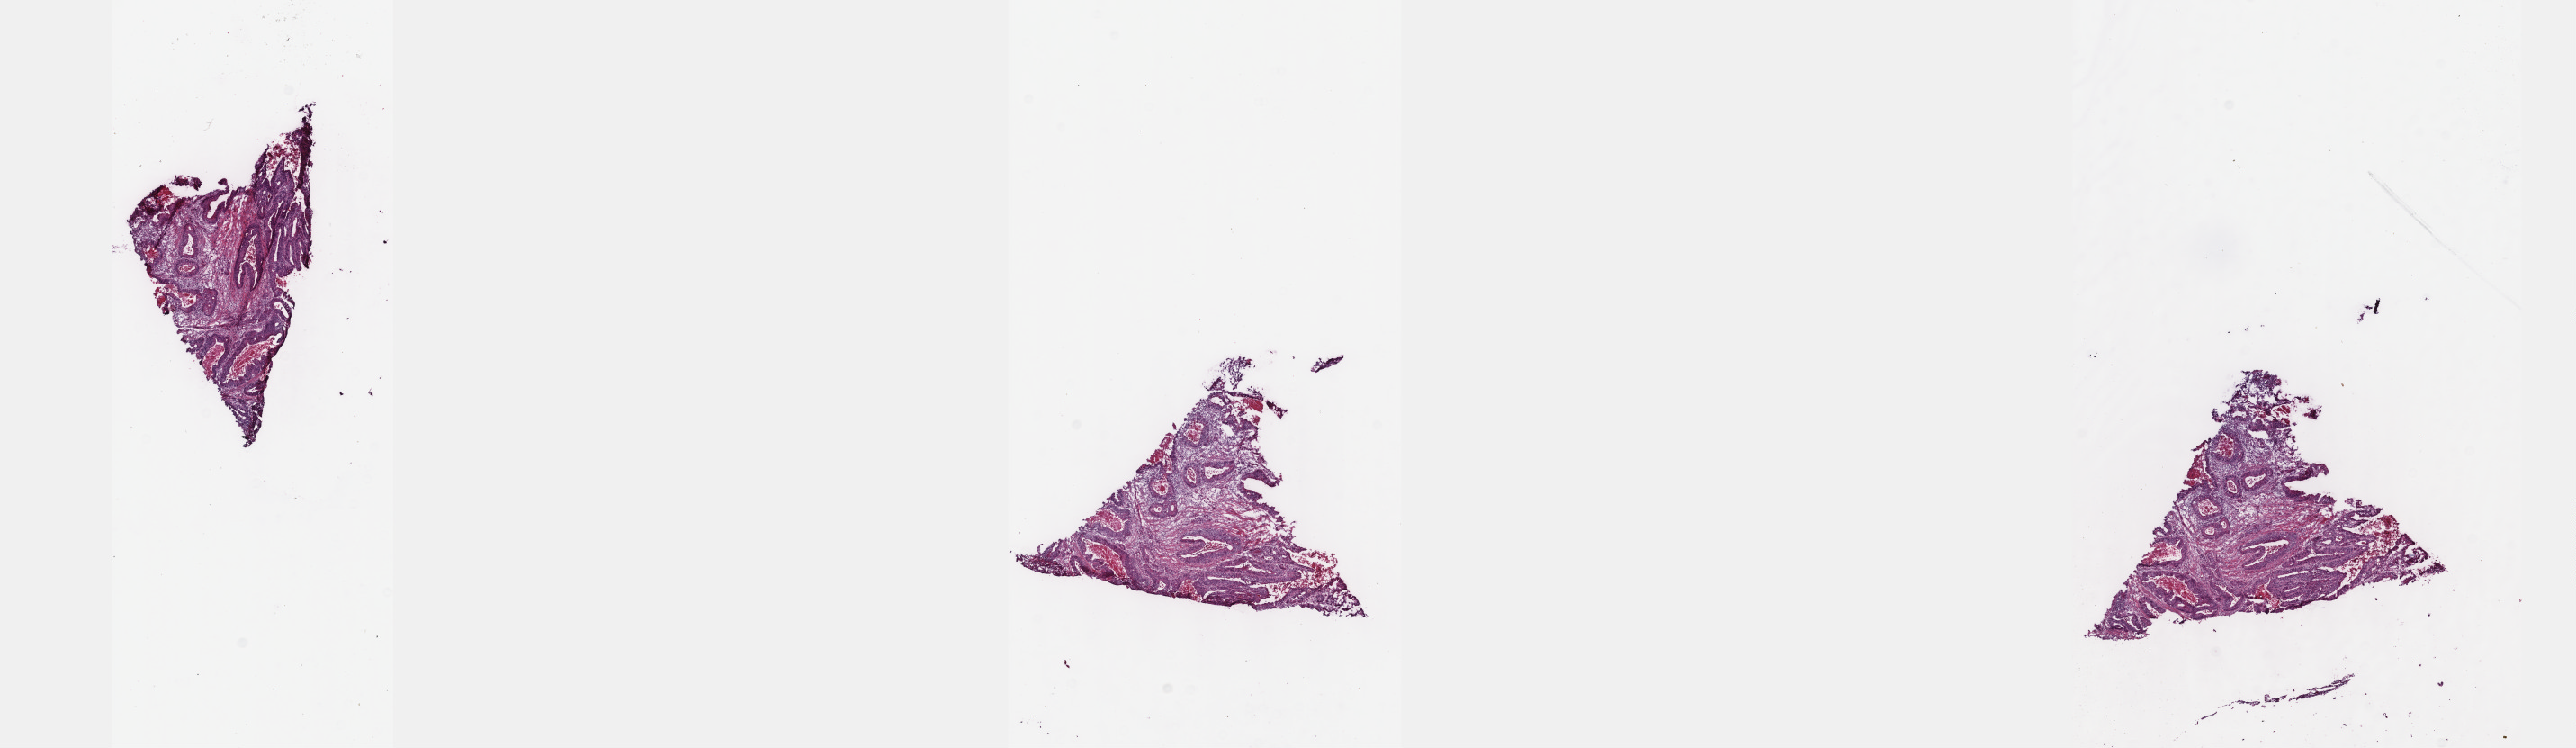
Digitized H&E tissue section (whole slide) — a low-resolution overview of the entire scanned area, about 23.1 x 6.7 mm. Frozen section. Primary tumour sample from the colon. Male patient; age at initial diagnosis 72 years. Slide review estimates, as recorded: tumour cells 80%, tumour nuclei 85%, normal cells 0%, stromal cells 18%, necrosis 2%. Inflammatory infiltration, as recorded: lymphocyte infiltration 8%, monocyte infiltration 2%, neutrophil infiltration 1%.
Lymph nodes positive (case pathology): 2 of 30 examined. AJCC pathologic stage: IIIB (6th edition). TNM: T3 N1 M0. Pathologic diagnosis: Adenocarcinoma, NOS (sigmoid colon).